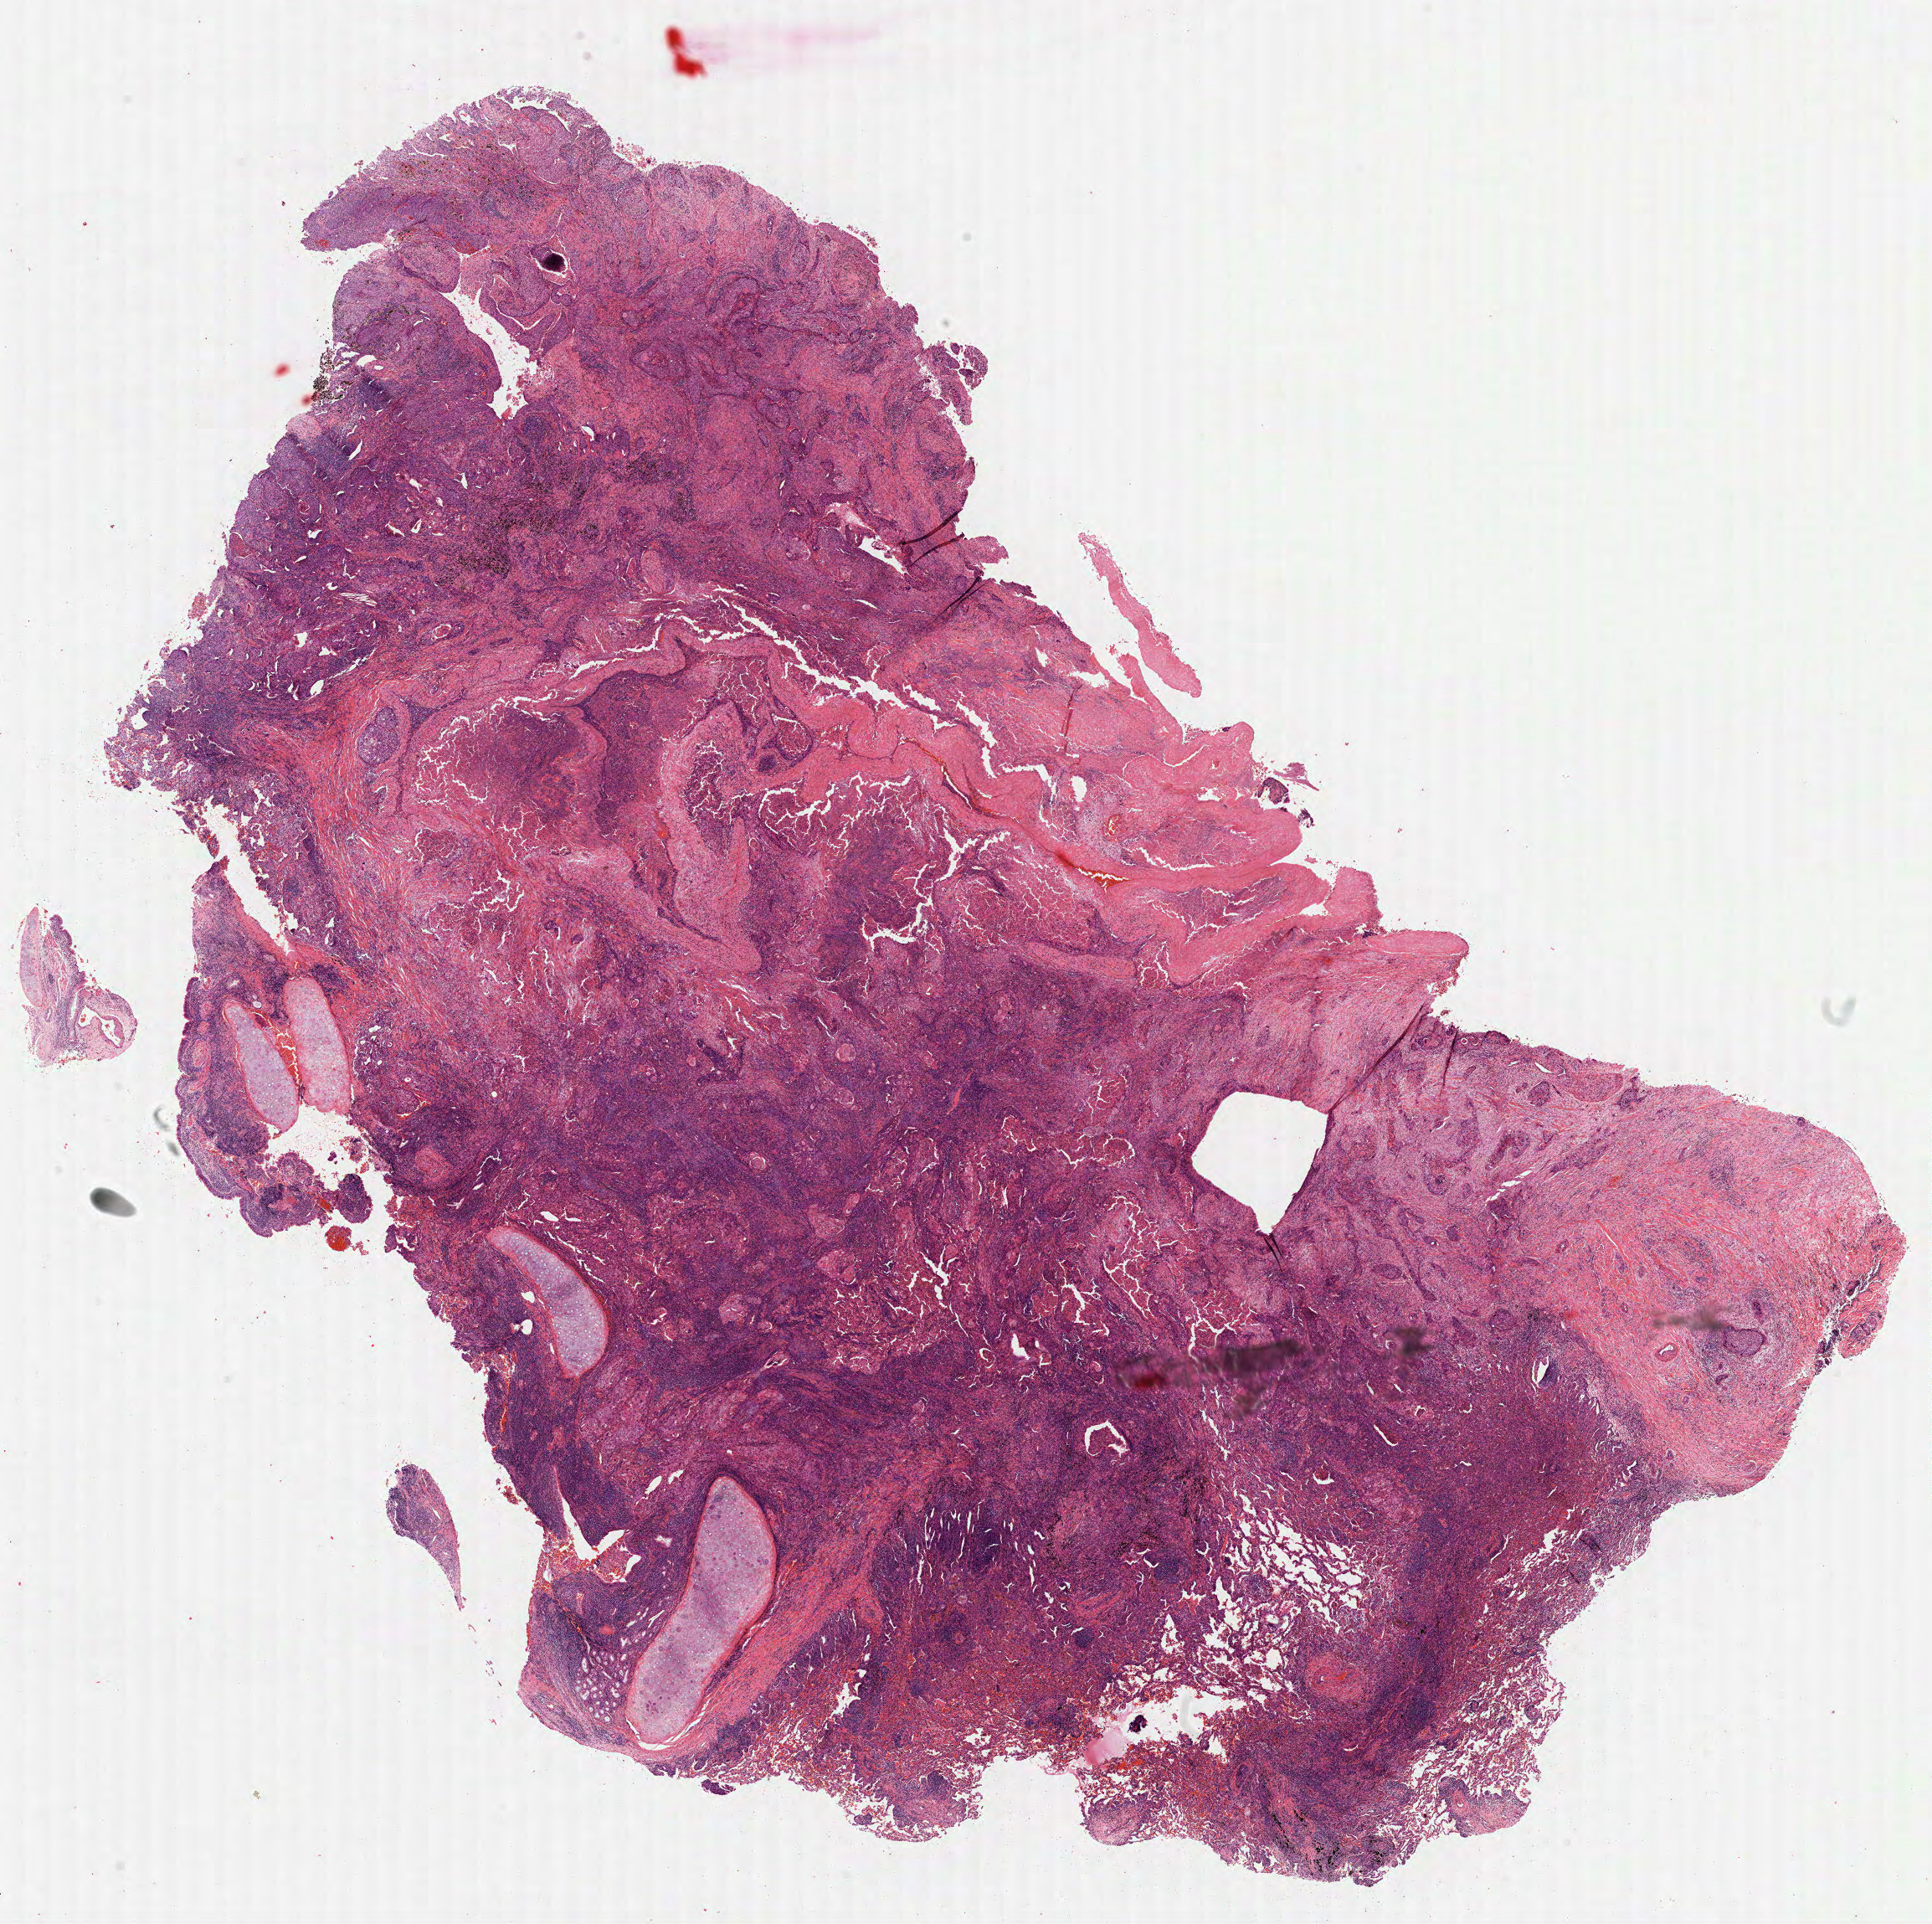
Whole-slide histology image, H&E — low-resolution overview of the scanned area, about 18.6 x 18.5 mm. Formalin-fixed paraffin-embedded (FFPE) diagnostic section. Lung, primary tumour sample. Male, age 49 years at initial diagnosis.
AJCC pathologic stage: IA (7th edition). TNM: T1a N0 M0. Diagnosis: Squamous cell carcinoma, keratinizing, NOS (upper lobe, lung).